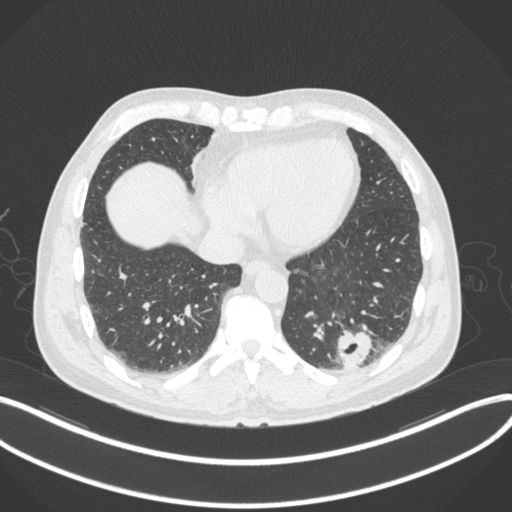
Chest CT, one axial slice; position 80 of 313 along the scan axis; lung window (W 1500 / L -600 HU); 512 × 512 image matrix. Patient: male, 54 years. From the clinical record (not read from this slice): clinical TNM (as recorded): T1c N0 M1.
Annotated regions visible in this slice (bounding box drawn by a radiologist):
- lung tumour (recorded histology: adenocarcinoma): bounding box (x1, y1, x2, y2) in pixels: (336, 326, 375, 368)